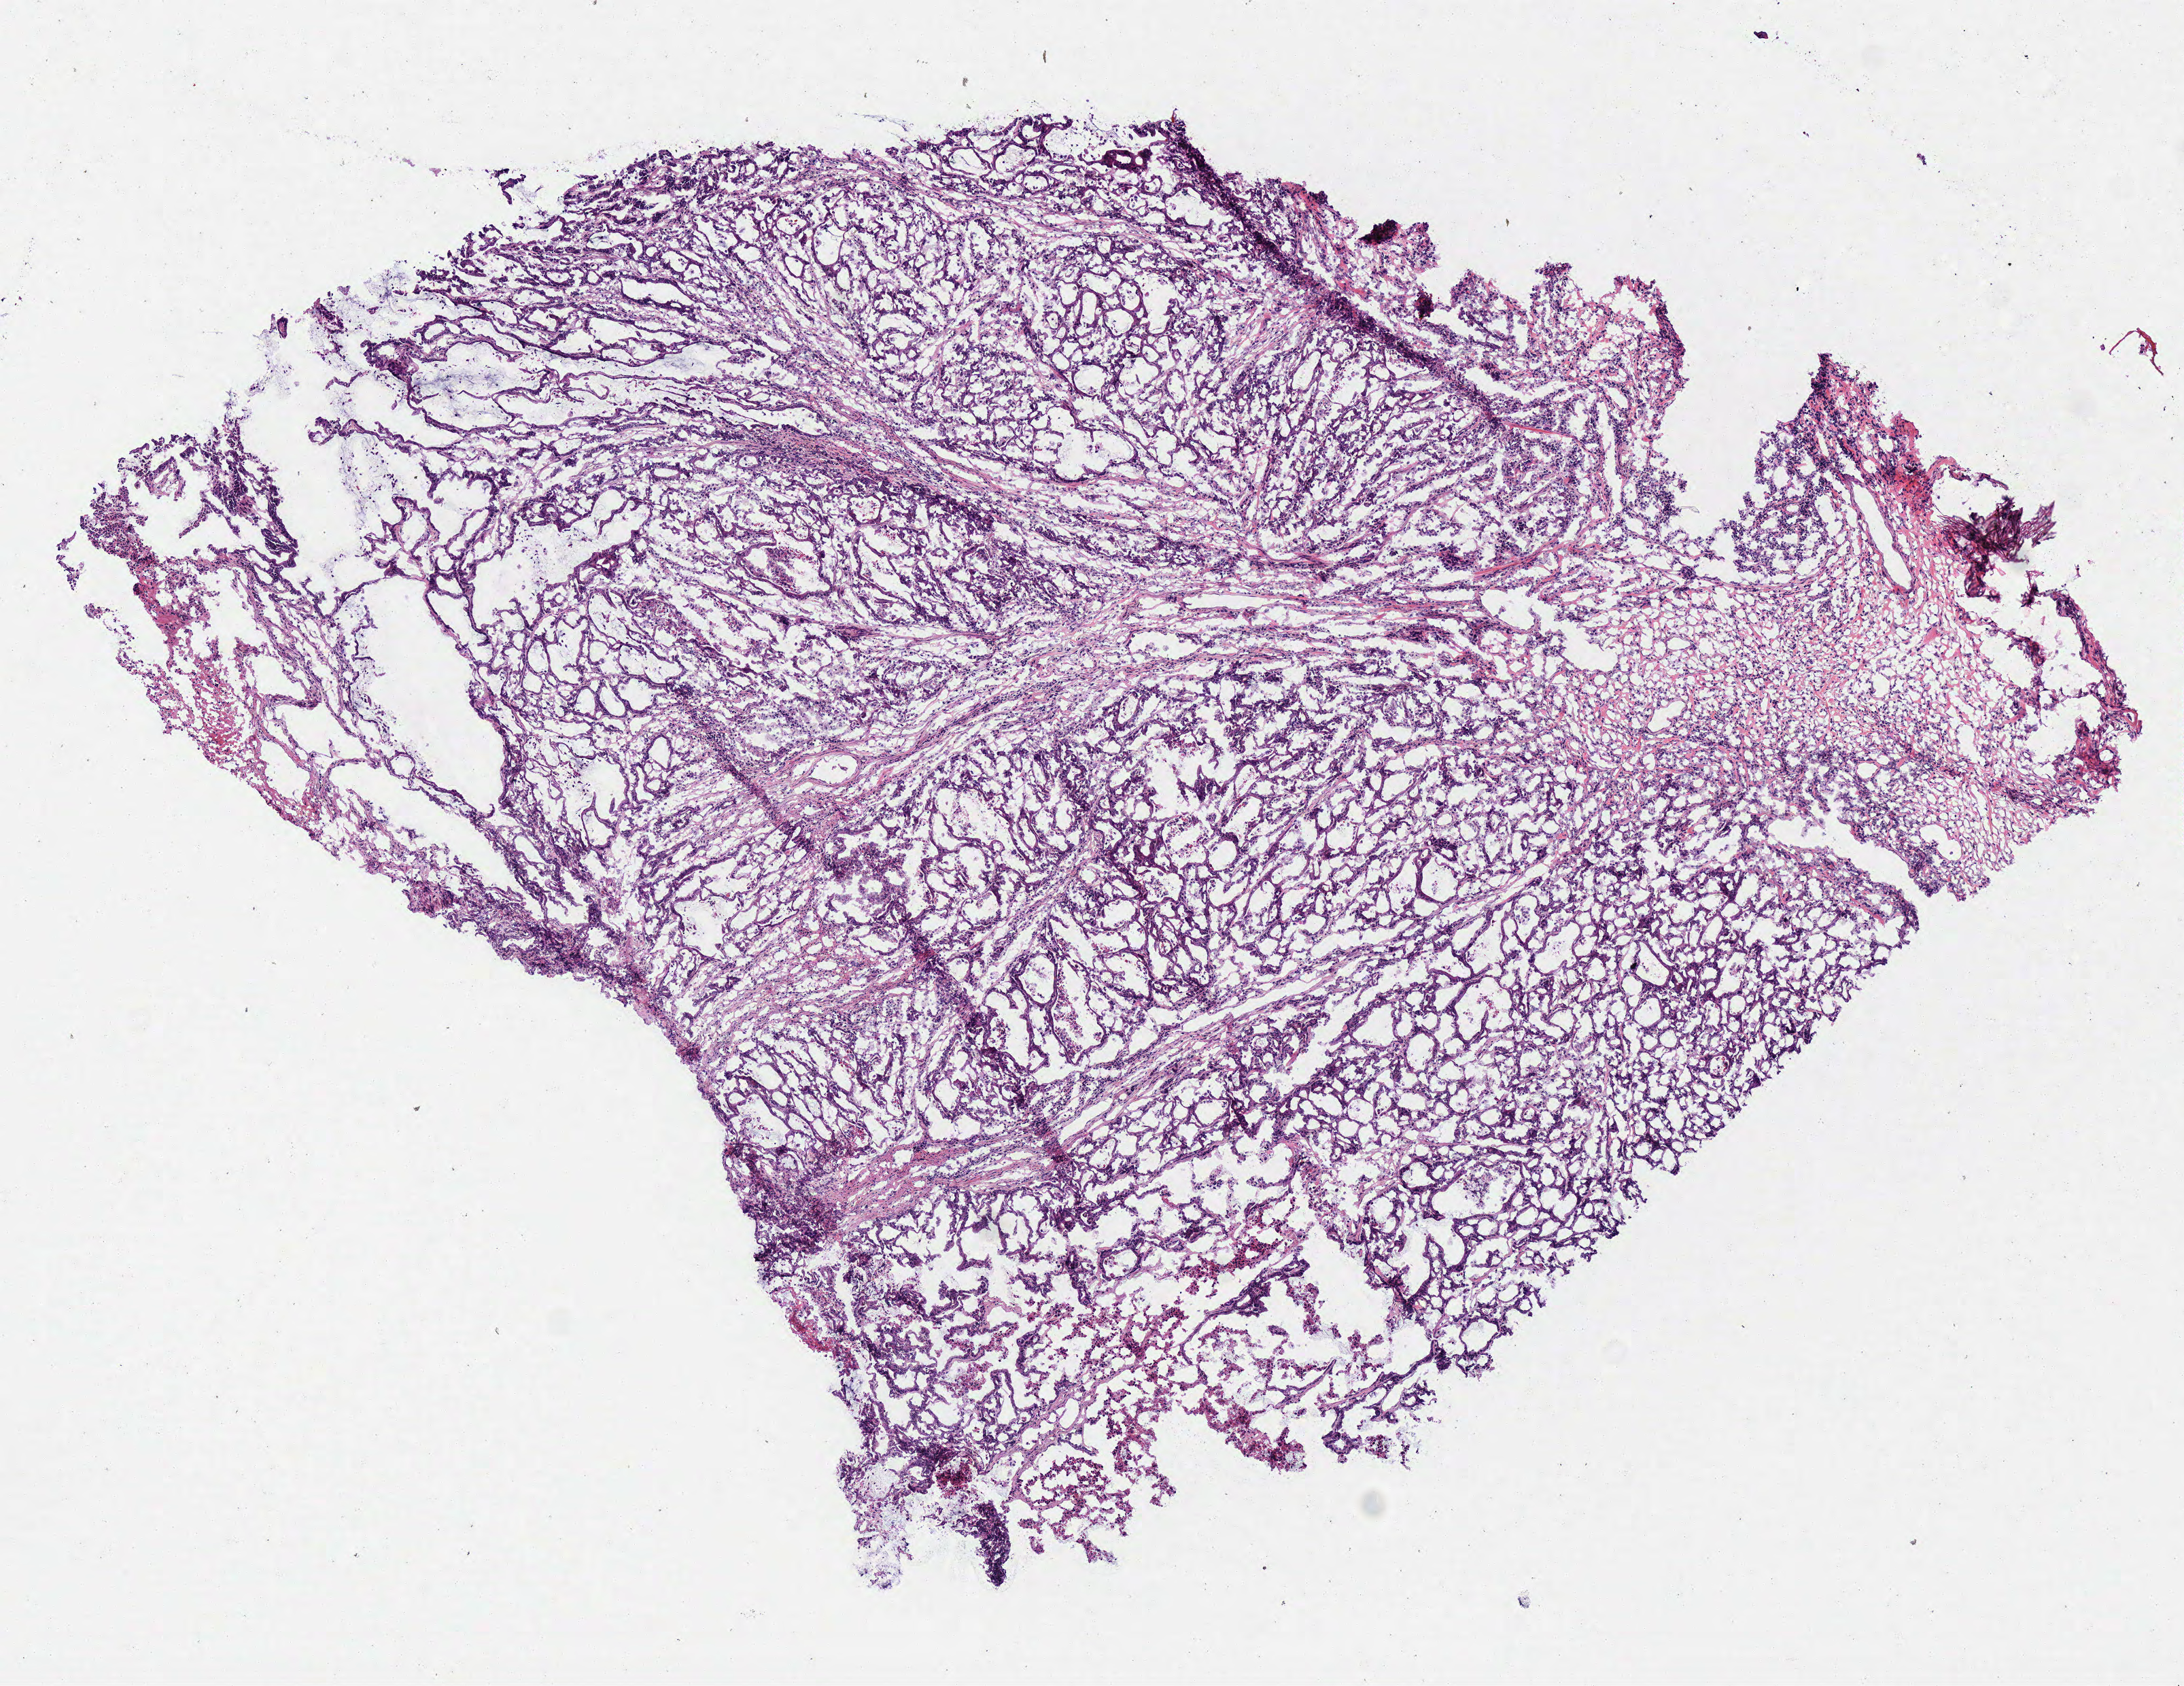
Whole-slide histology image, H&E, shown as a low-resolution overview of the whole scanned area (about 6.3 x 4.9 mm), frozen section from the bottom of the tissue portion, primary tumour sample from the colon. Female patient; age at initial diagnosis 73 years. Slide review estimates, as recorded: tumour cells 90%, tumour nuclei 75%, normal cells 0%, stromal cells 15%, necrosis 5%.
AJCC pathologic stage: IIA. Histologic diagnosis: Adenocarcinoma, NOS. TNM: T3 N0 M0. Lymph nodes positive (case pathology): 0 of 17 examined.